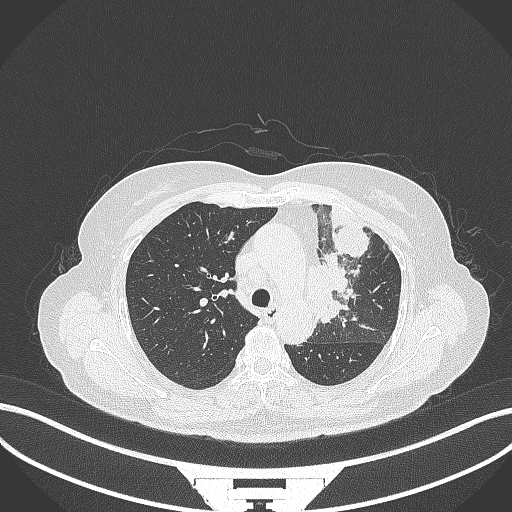
Chest CT, one axial slice. Slice 233 of 382 in the series (ordered by position). Reconstruction kernel B70f. 120 kVp. Lung window (W 1500 / L -600 HU). 1 mm slice thickness. 512 × 512 image matrix. Female patient, age 64 years. From the clinical record (not read from this slice): clinical TNM (as recorded): T2a N2 M0.
Annotated regions visible in this slice (bounding box drawn by a radiologist):
- lung tumour (recorded histology: adenocarcinoma): bounding box <303,247,352,328> (left, top, right, bottom; pixels)
- lung tumour (recorded histology: adenocarcinoma): <330,220,370,260>